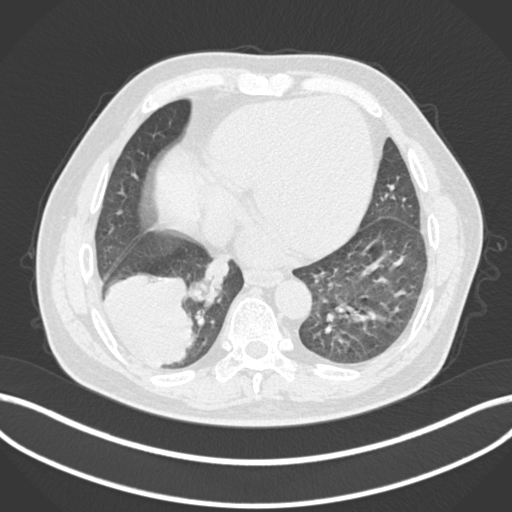
Chest CT, one axial slice; position 46 of 200 along the scan axis; reconstruction kernel B30f; 120 kVp; lung window (W 1500 / L -600 HU); 1 mm slice thickness; 512 × 512 image matrix. Patient: male, 59 years.
Annotated regions visible in this slice (bounding box drawn by a radiologist):
- lung tumour (recorded histology: adenocarcinoma): box from (x=98, y=271) to (x=198, y=372) px